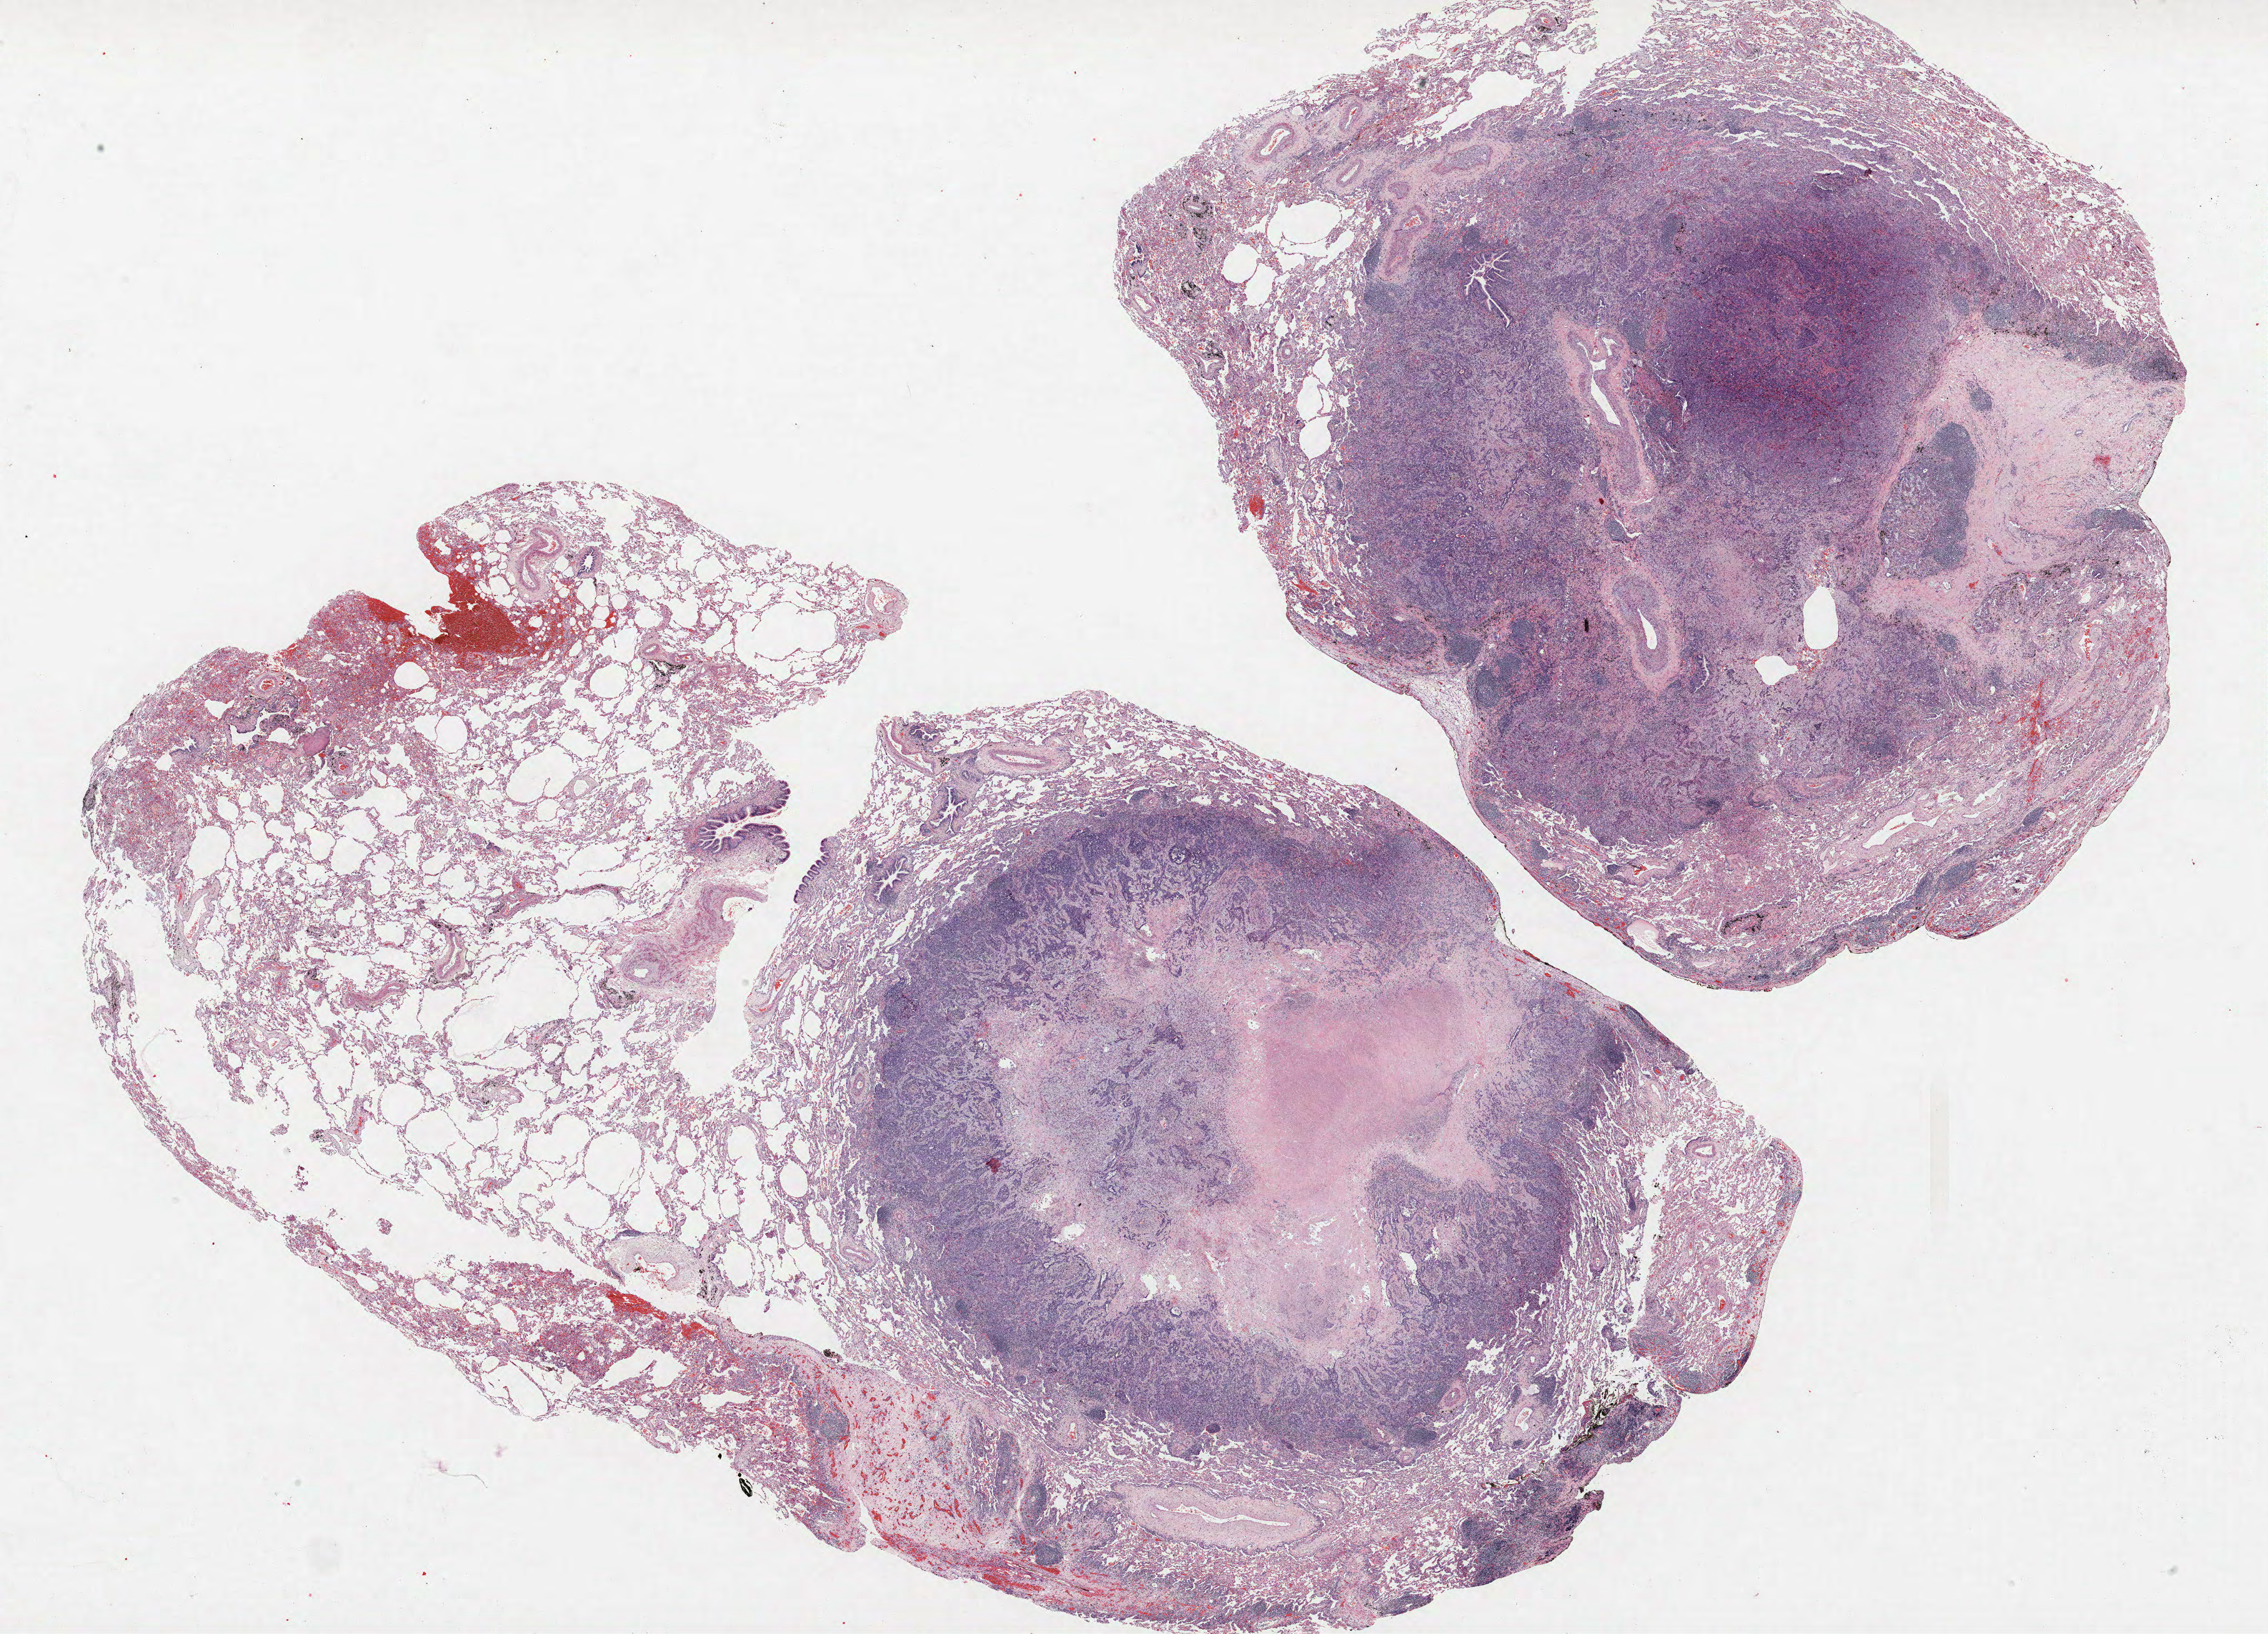
Whole-slide histology image, Hematoxylin and eosin (H&E) stained, shown as a low-resolution overview of the whole scanned area (about 29.0 x 20.9 mm, from a 40x scan); formalin-fixed paraffin-embedded (FFPE) section; lung tissue. Male patient, aged 62 at enrolment. Former smoker at enrolment. Grade: poorly differentiated (G3).
Primary tumour location (clinical record): right lower lobe. Stage (AJCC 6th edition): IV. ICD-O-3 topography: lower lobe of lung (C34.3). Participant's lung-cancer diagnosis: Adenocarcinoma, NOS. Tumour size (pathology): 15 mm.